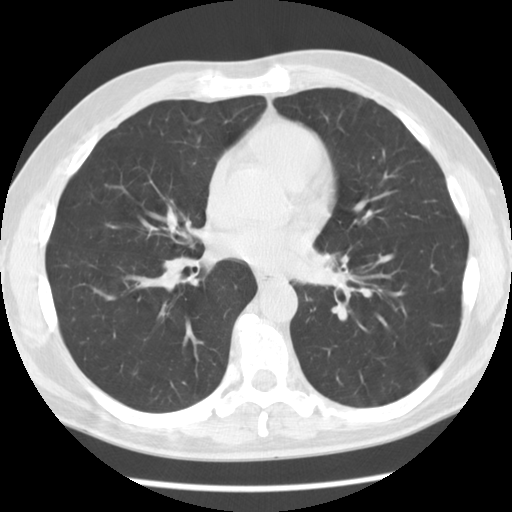
Chest CT (low-dose screening protocol), one axial image; baseline annual screen; lung window (W 1500 / L -600 HU); standard (soft-tissue) reconstruction kernel (STANDARD); 120 kVp; slice 62 of 112 in the series. Male participant, aged 55 years at enrolment. Former smoker at enrolment.
Expert-annotated lung lesion, bounding box (x1, y1, x2, y2) in pixels: (280, 235, 349, 305). No non-calcified nodule or mass ≥4 mm was recorded by the screening reader at this exam. Official screen result: negative screen, minor abnormalities not suspicious for lung cancer. Later outcome: lung cancer diagnosed 223 days after this screen — squamous cell carcinoma, NOS, left lower lobe, moderately differentiated (G2), stage IV (AJCC 6th edition), 51 mm at pathology.